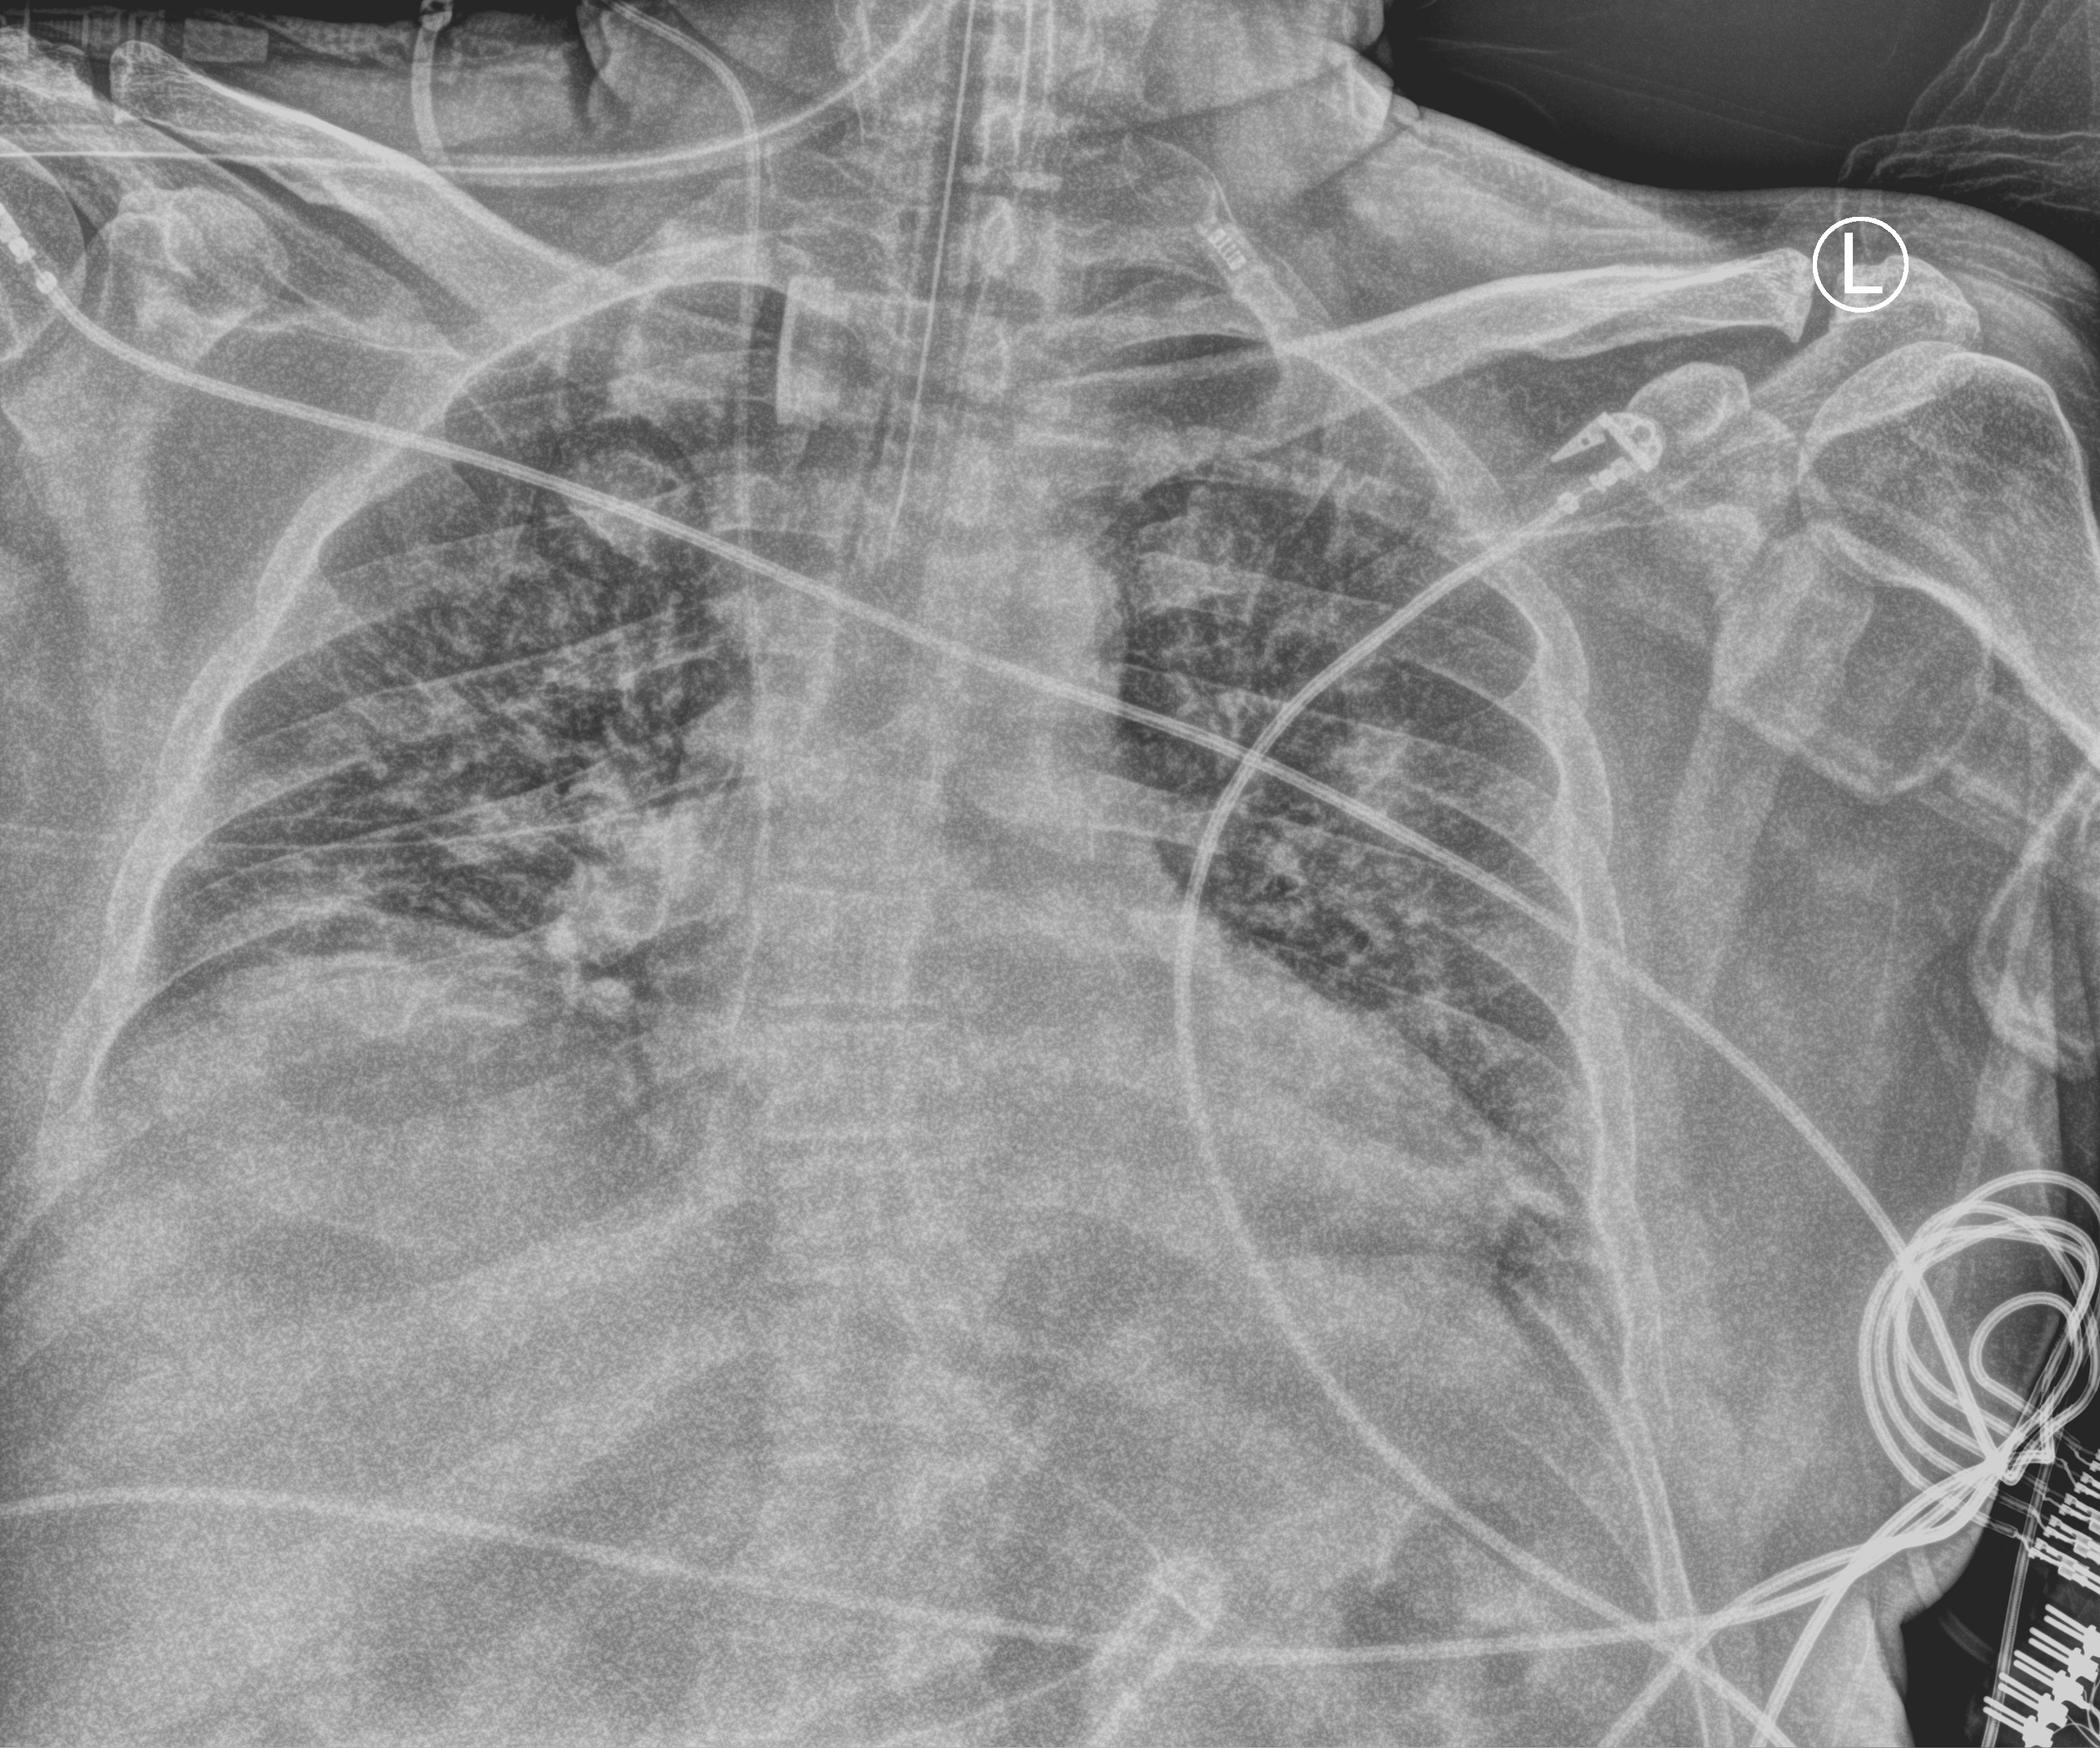
Chest X-ray (portable); anteroposterior (AP) projection. Patient hospitalised with COVID-19; male, aged 18–59 years.
From the hospital-stay record, not from the radiograph (when in the stay this image was taken is not recorded): length of hospital stay: 17 days.